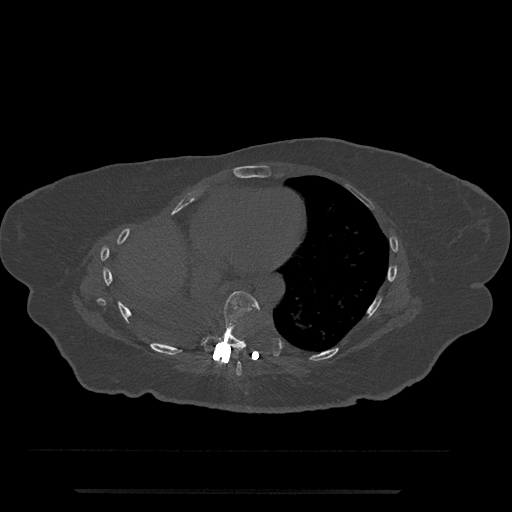
CT including the spine, one axial slice; reconstruction kernel Br40s/3; 120 kVp; bone window (W 1800 / L 400 HU); 0.5 mm slice thickness; 512 × 512 image matrix, field of view 440 × 440 mm. Female patient, age 51 years. From the clinical record (not read from this slice): primary cancer: neuro.
Outlined on this slice (semi-automatic segmentation, software-assisted and operator-edited):
- T7 vertebra: bounding box [x1, y1, x2, y2] px = [233, 362, 242, 376]
- T8 vertebra: [201, 291, 260, 352]